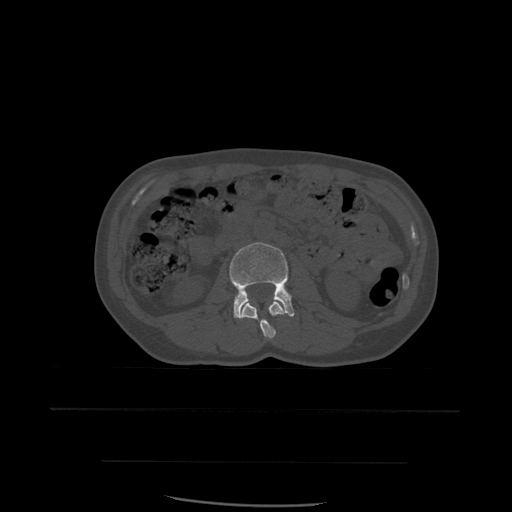
CT including the spine, one axial slice. Bone window (W 1800 / L 400 HU). 1.25 mm slice thickness. 512 × 512 image matrix, field of view 392 × 392 mm. Patient age 48 years. From the clinical record (not read from this slice): primary cancer: lung; vertebrae with lytic lesions (as recorded): T11.
Structures marked on this image (semi-automatic segmentation, software-assisted and operator-edited):
- L2 vertebra: bounding box <239,302,285,339> (left, top, right, bottom; pixels)
- L3 vertebra: <229,243,295,319>